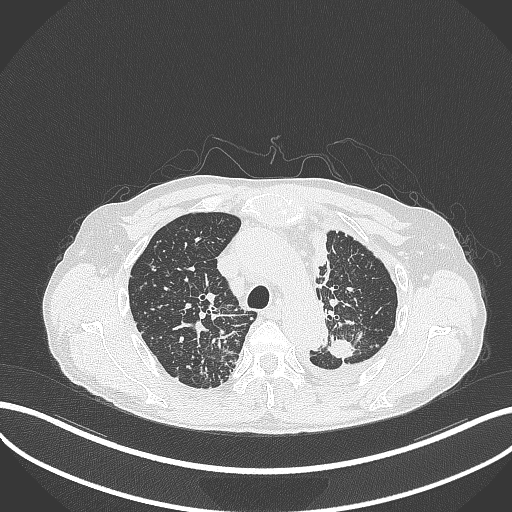
Chest CT, one axial slice; position 264 of 325 along the scan axis; lung window (W 1500 / L -600 HU); 1 mm slice thickness; 512 × 512 image matrix, field of view 400 × 400 mm. Male patient, age 58 years. From the clinical record (not read from this slice): clinical TNM (as recorded): T1c N3 M1.
Structures marked on this image (rectangle marked by the reading radiologist):
- lung tumour (recorded histology: adenocarcinoma): bounding box <320,330,358,361> (left, top, right, bottom; pixels)